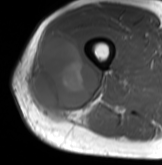
MRI of an extremity soft-tissue mass, one axial slice; slice 38 of 61 in the series (ordered by position); MR volume resampled by the dataset authors to the PET/CT grid (not the native acquisition matrix); 3.27 mm slice thickness; 162 × 165 image matrix, field of view 158 × 161 mm. Male patient. From the clinical record (not read from this slice): histological type: poorly differentiated synovial sarcoma; grade: high; site of the primary tumour: right buttock.
Annotated regions visible in this slice (expert contour drawn on MRI and transferred to this co-registered scan by the dataset authors):
- gross tumour volume including surrounding oedema: box from (x=32, y=34) to (x=99, y=119) px
- gross tumour volume (mass): (x=34, y=34)–(x=99, y=119)